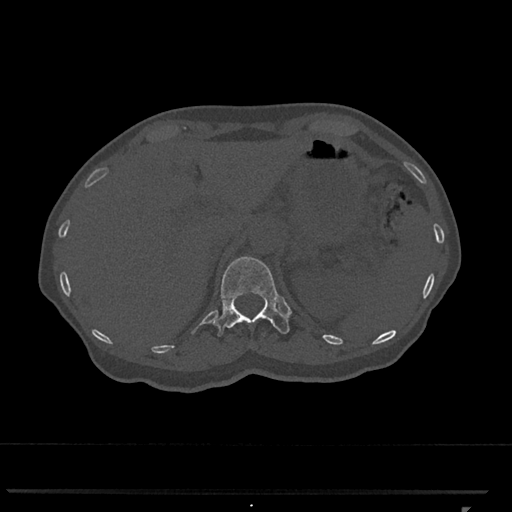
CT including the spine, one axial slice; slice 466 of 793 in the series (ordered by position); reconstruction kernel Br40s/3; 120 kVp; bone window (W 1800 / L 400 HU); 512 × 512 image matrix. Female patient, age 62 years. Case-level facts recorded for this patient, not image findings: primary cancer: renal.
Annotated regions visible in this slice (semi-automatically segmented with operator editing):
- T12 vertebra: box from (x=212, y=256) to (x=290, y=336) px